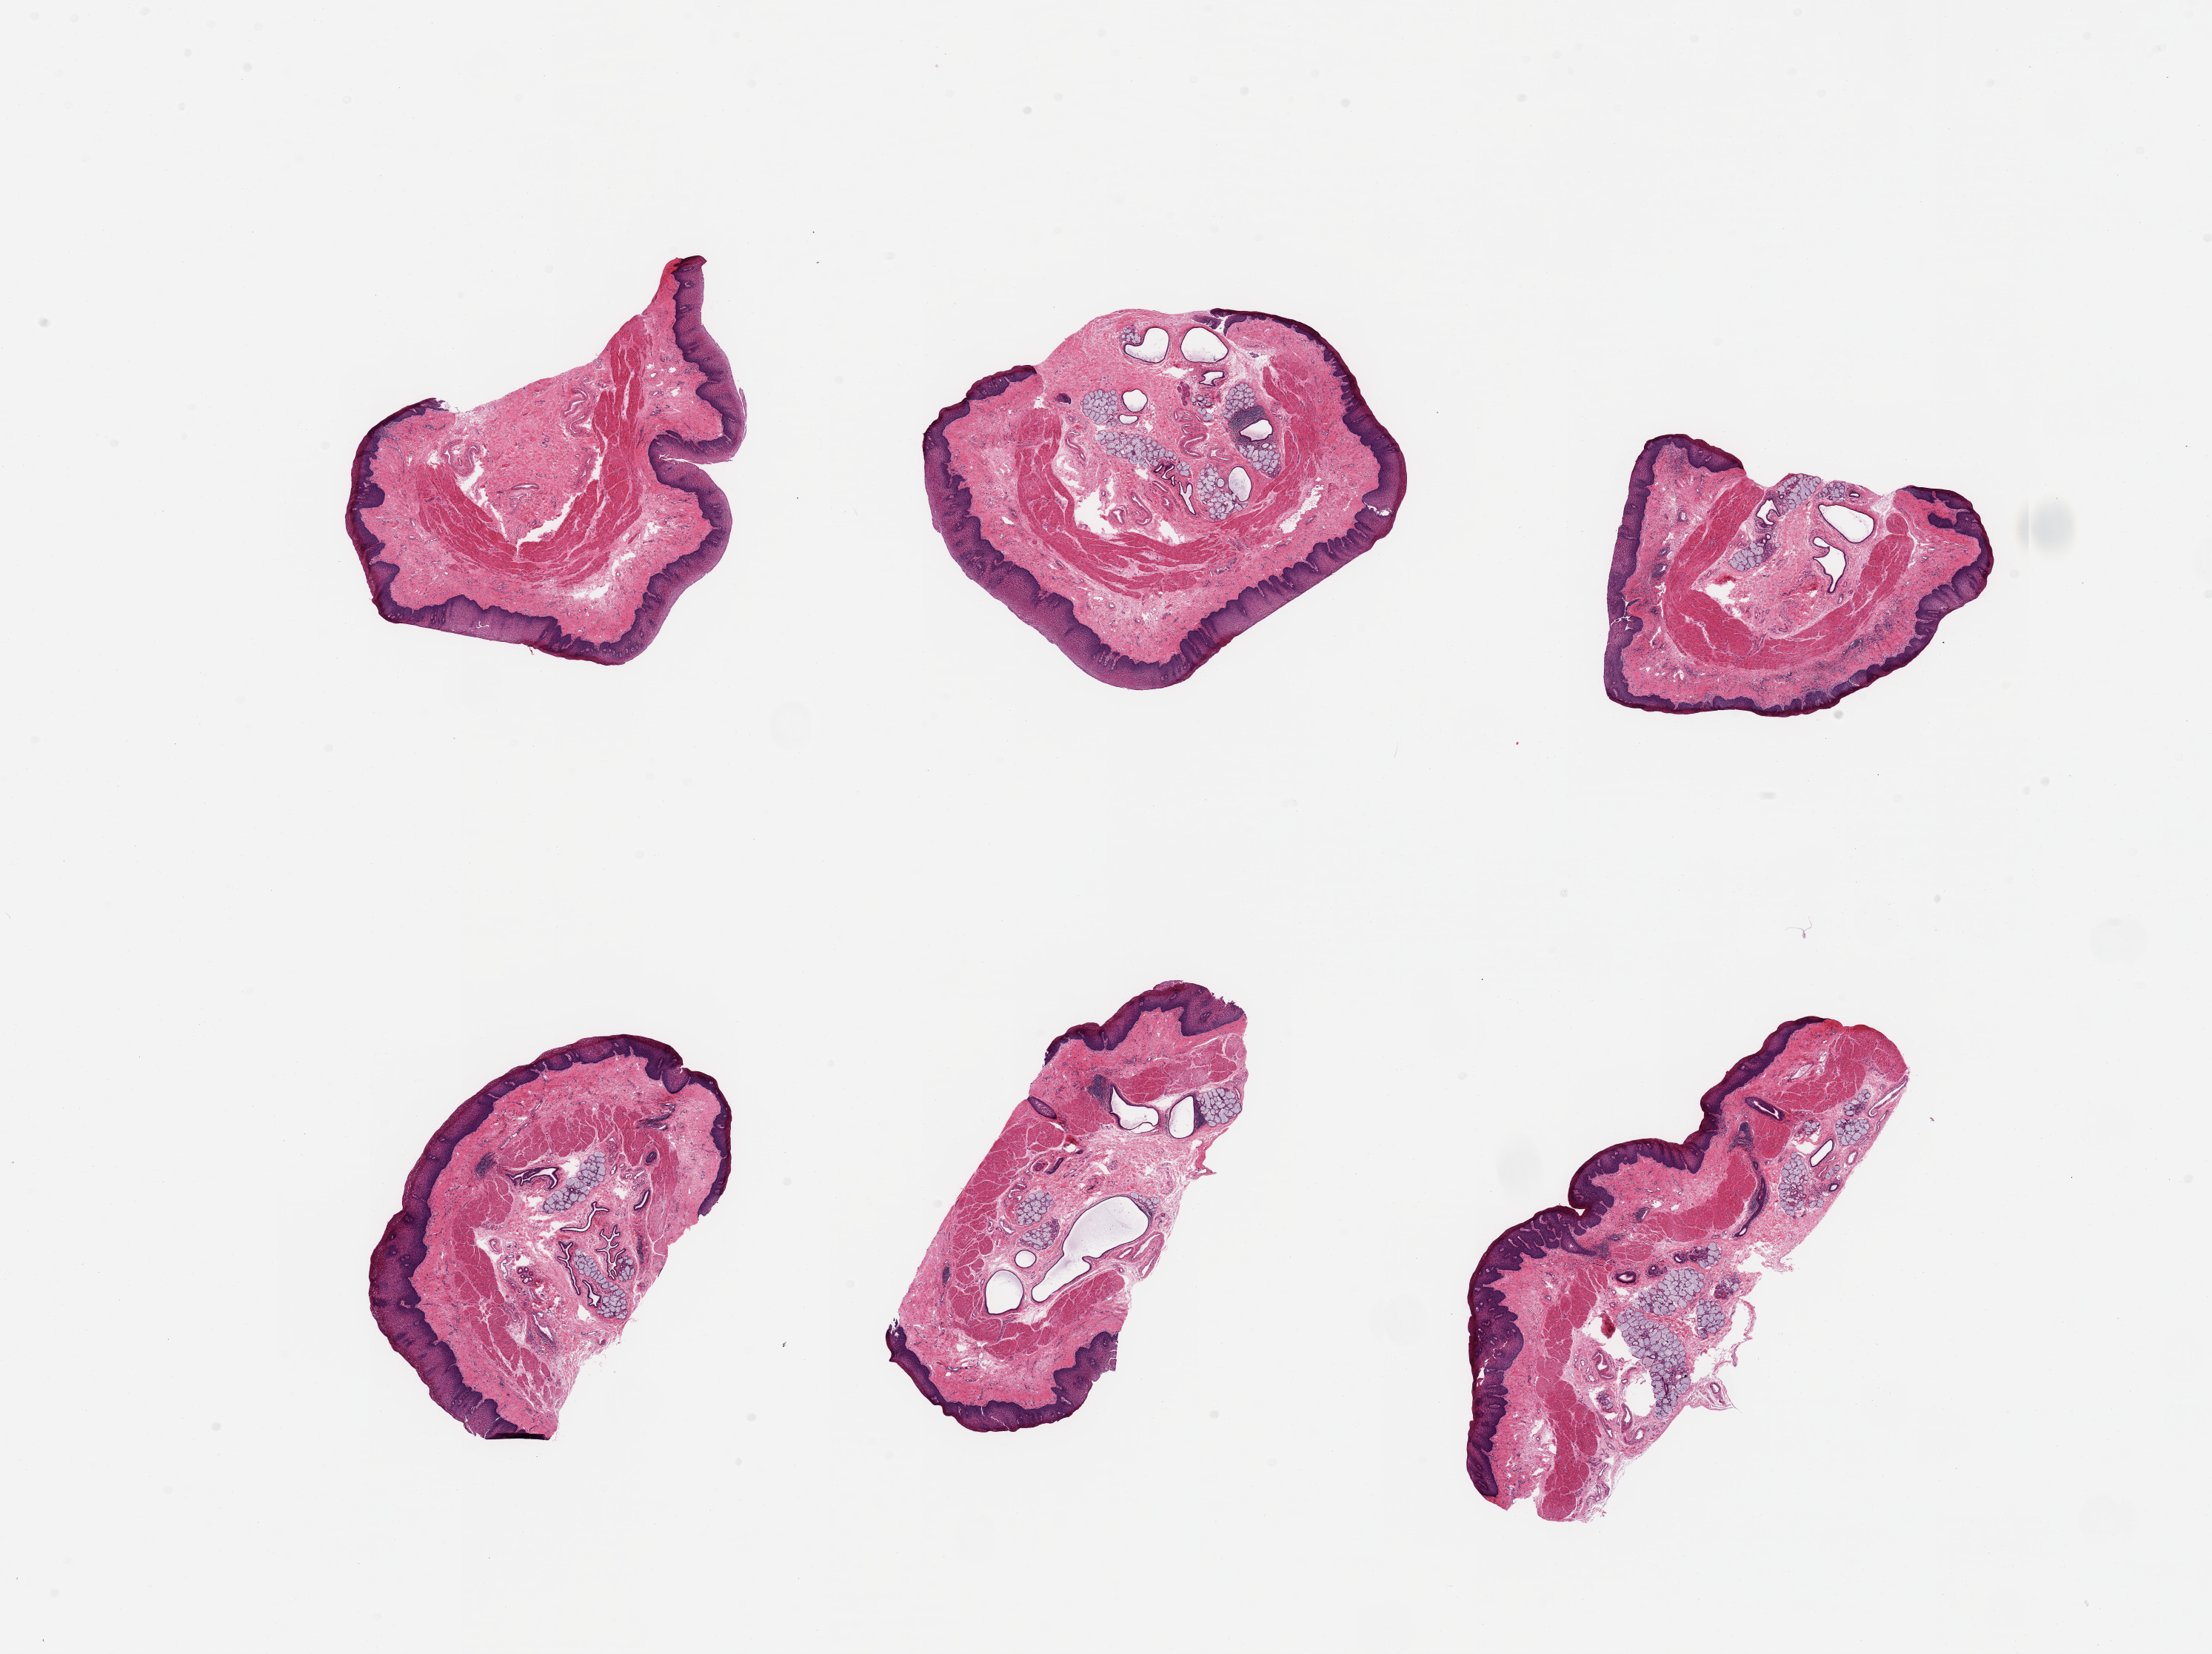
Whole-slide image, H&E stain, brightfield, whole scanned area (about 23.6 x 17.7 mm) shown as a low-resolution overview, PAXgene-fixed paraffin-embedded (PFPE) section, sampled site (target tissue): esophageal mucous membrane, tissue donor sample. Donor: female.
Review note (as recorded): 6 pieces, squamous mucosa up to ~0.4mm, ~20% thickness; submucosal mucus glands numerous.